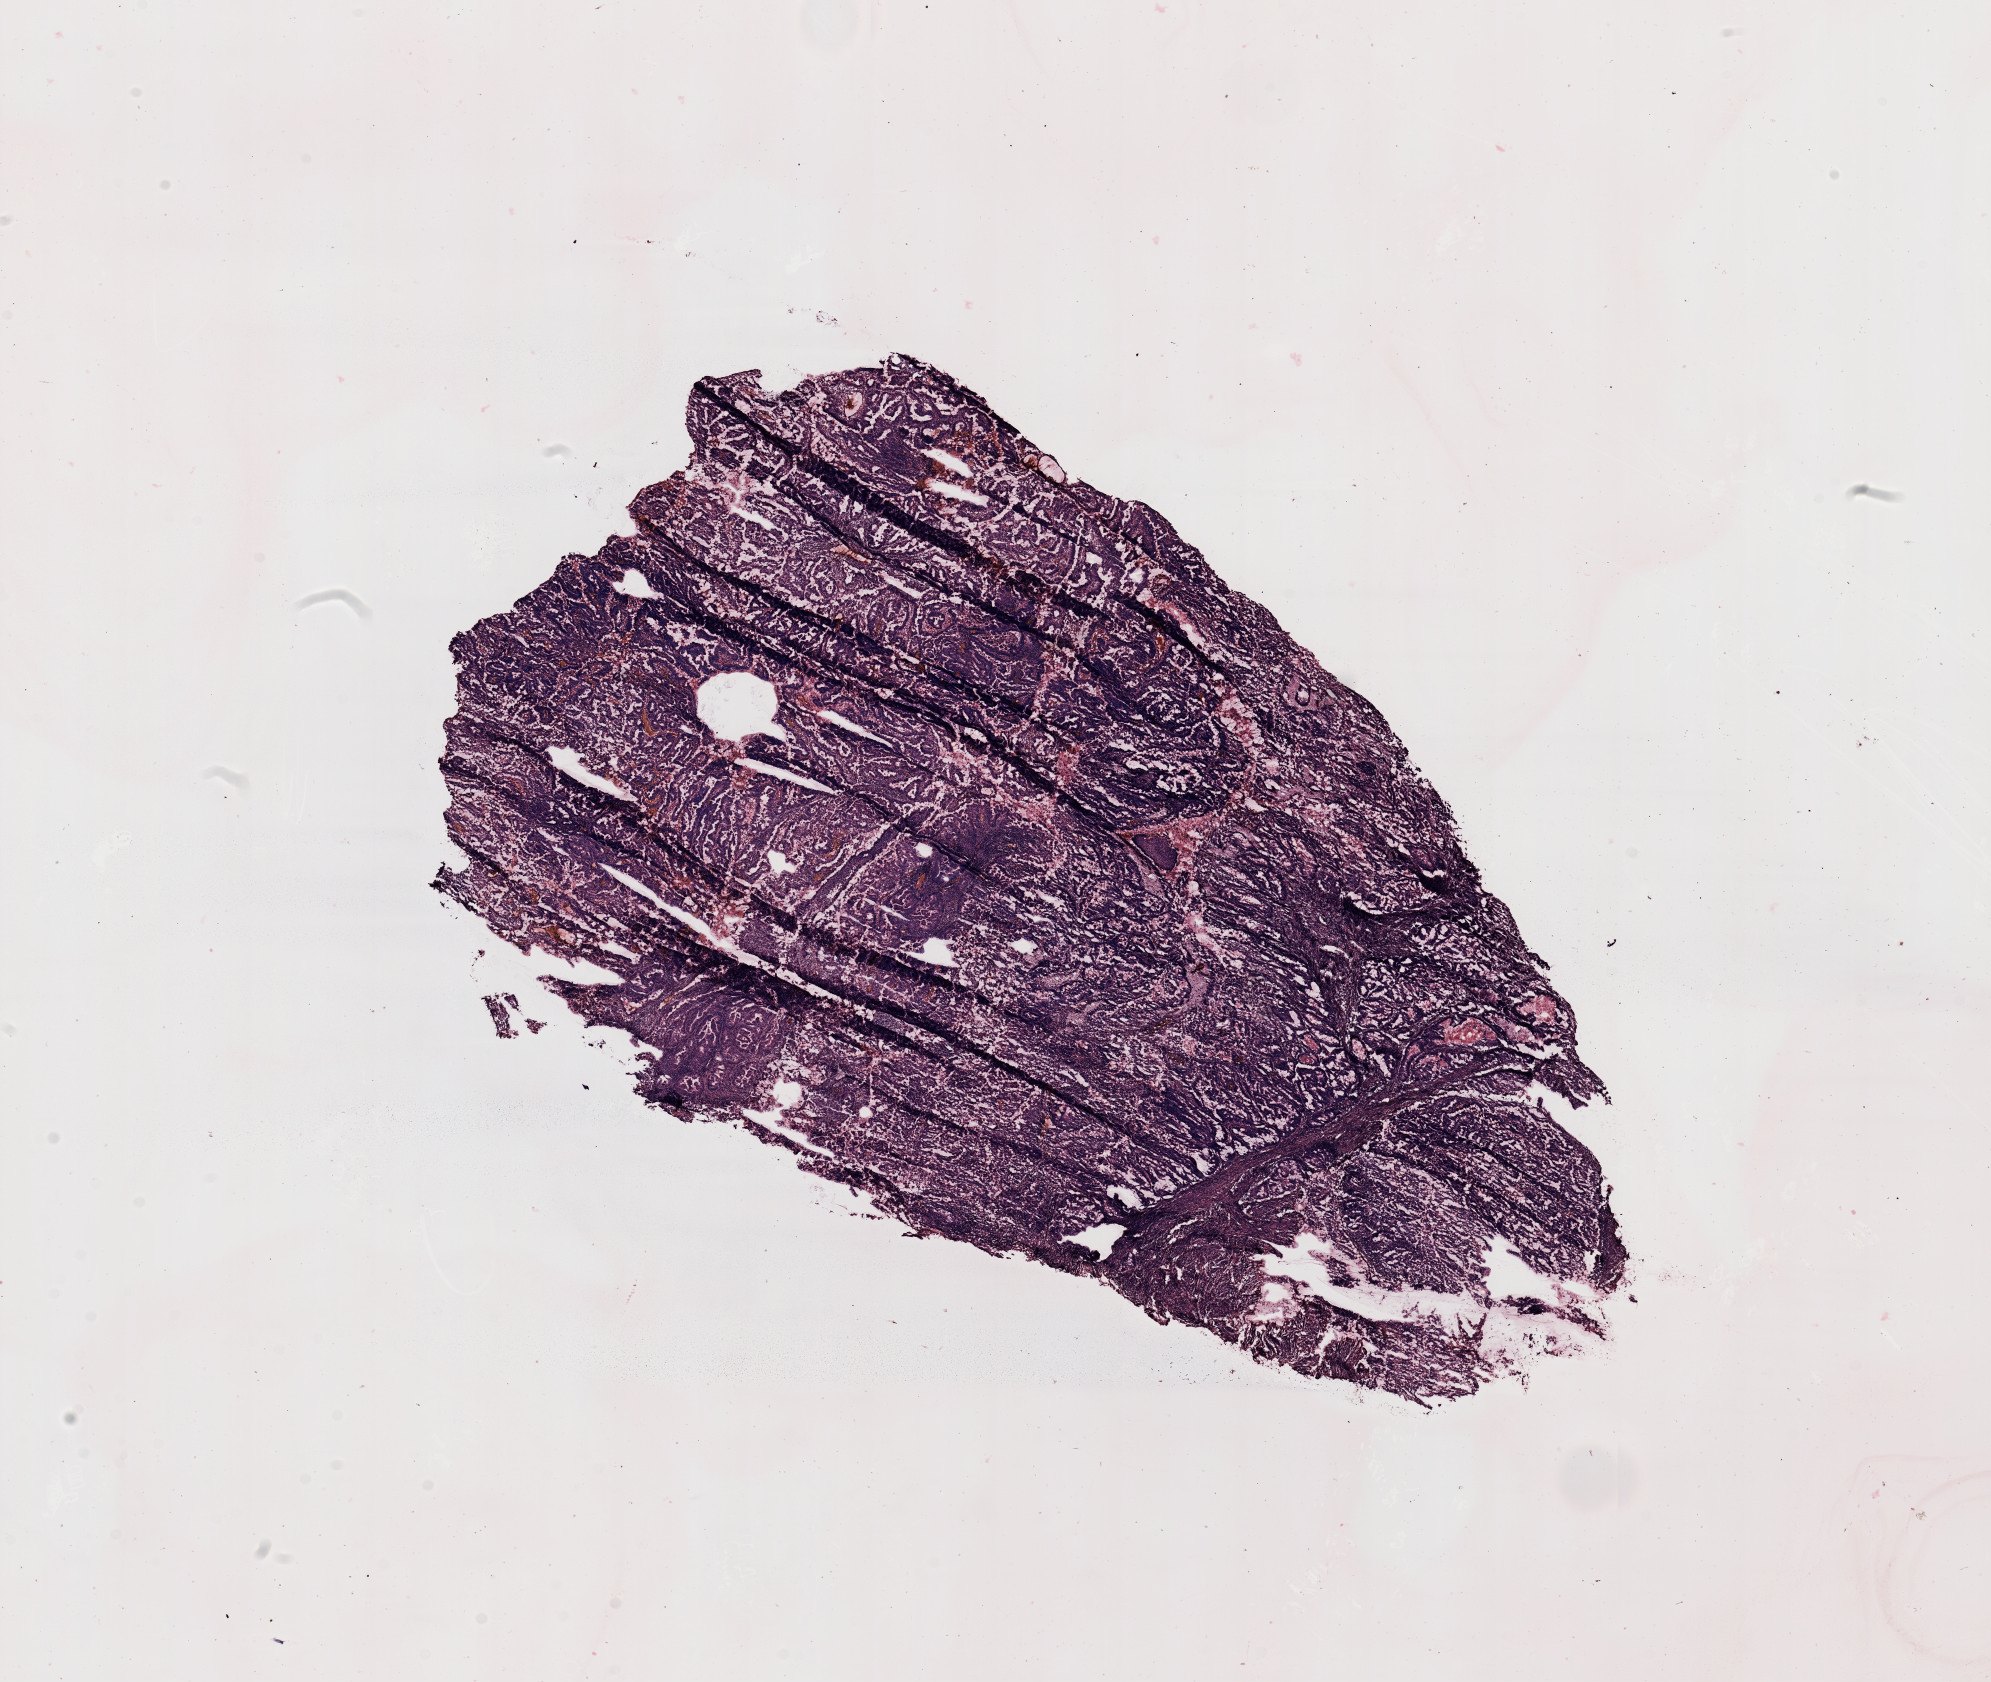
Digitized H&E-stained tissue section (whole slide) — shown as a low-resolution overview of the whole scanned area (about 15.8 x 13.3 mm, from a 20x scan). Tumour tissue sample, sampled site: uterus. 66-year-old female patient. Histologic grade: G2 (moderately differentiated). Composition of this section per pathologist review: tumour nuclei 95%, necrosis 5%.
Diagnosis: Endometrioid adenocarcinoma, NOS. AJCC pathologic stage: II.